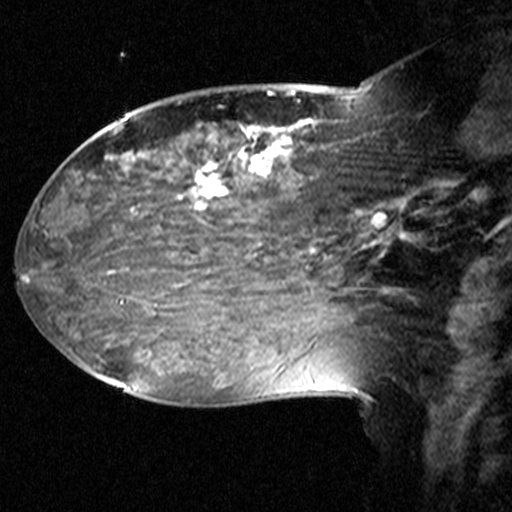
Breast MRI (dynamic contrast-enhanced), one sagittal slice. Slice 20 of 44 in the series (ordered by position). Dynamic contrast-enhanced study with each time point stored as its own series, time point 2 of 3 at this slice position (early post-contrast, ordered by acquisition time). 1.5 T. TE 4.5 ms, TR 11 ms. 3 mm slice thickness. 512 × 512 image matrix, field of view 240 × 240 mm. Female patient, age 38 years. Case-level facts recorded for this patient, not image findings: setting: breast cancer imaged before/during neoadjuvant chemotherapy; receptor status: HR-positive, HER2-negative.
Structures marked on this image (semi-automatic segmentation, software-assisted and operator-edited):
- analysis volume of interest (the breast-tissue region the enhancement analysis was run in; not a lesion): bounding box <124,106,405,245> (left, top, right, bottom; pixels)
- tumour enhancement mask (voxels above the 90 % enhancement threshold inside the analysis volume of interest): <181,126,381,225>